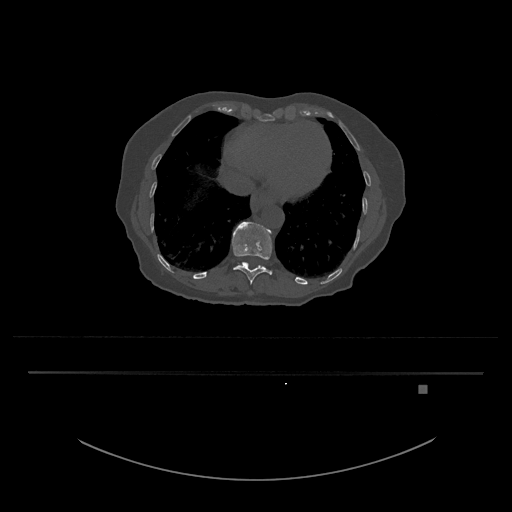
CT including the spine, one axial slice; position 659 of 797 along the scan axis; bone window (W 1800 / L 400 HU); 512 × 512 image matrix, field of view 500 × 500 mm. Patient: female, 57 years. Case-level facts recorded for this patient, not image findings: primary cancer: cervical.
Outlined on this slice (semi-automatic segmentation, software-assisted and operator-edited):
- T11 vertebra: bounding box (x1, y1, x2, y2) in pixels: (232, 221, 273, 284)
- T12 vertebra: (237, 262, 266, 269)